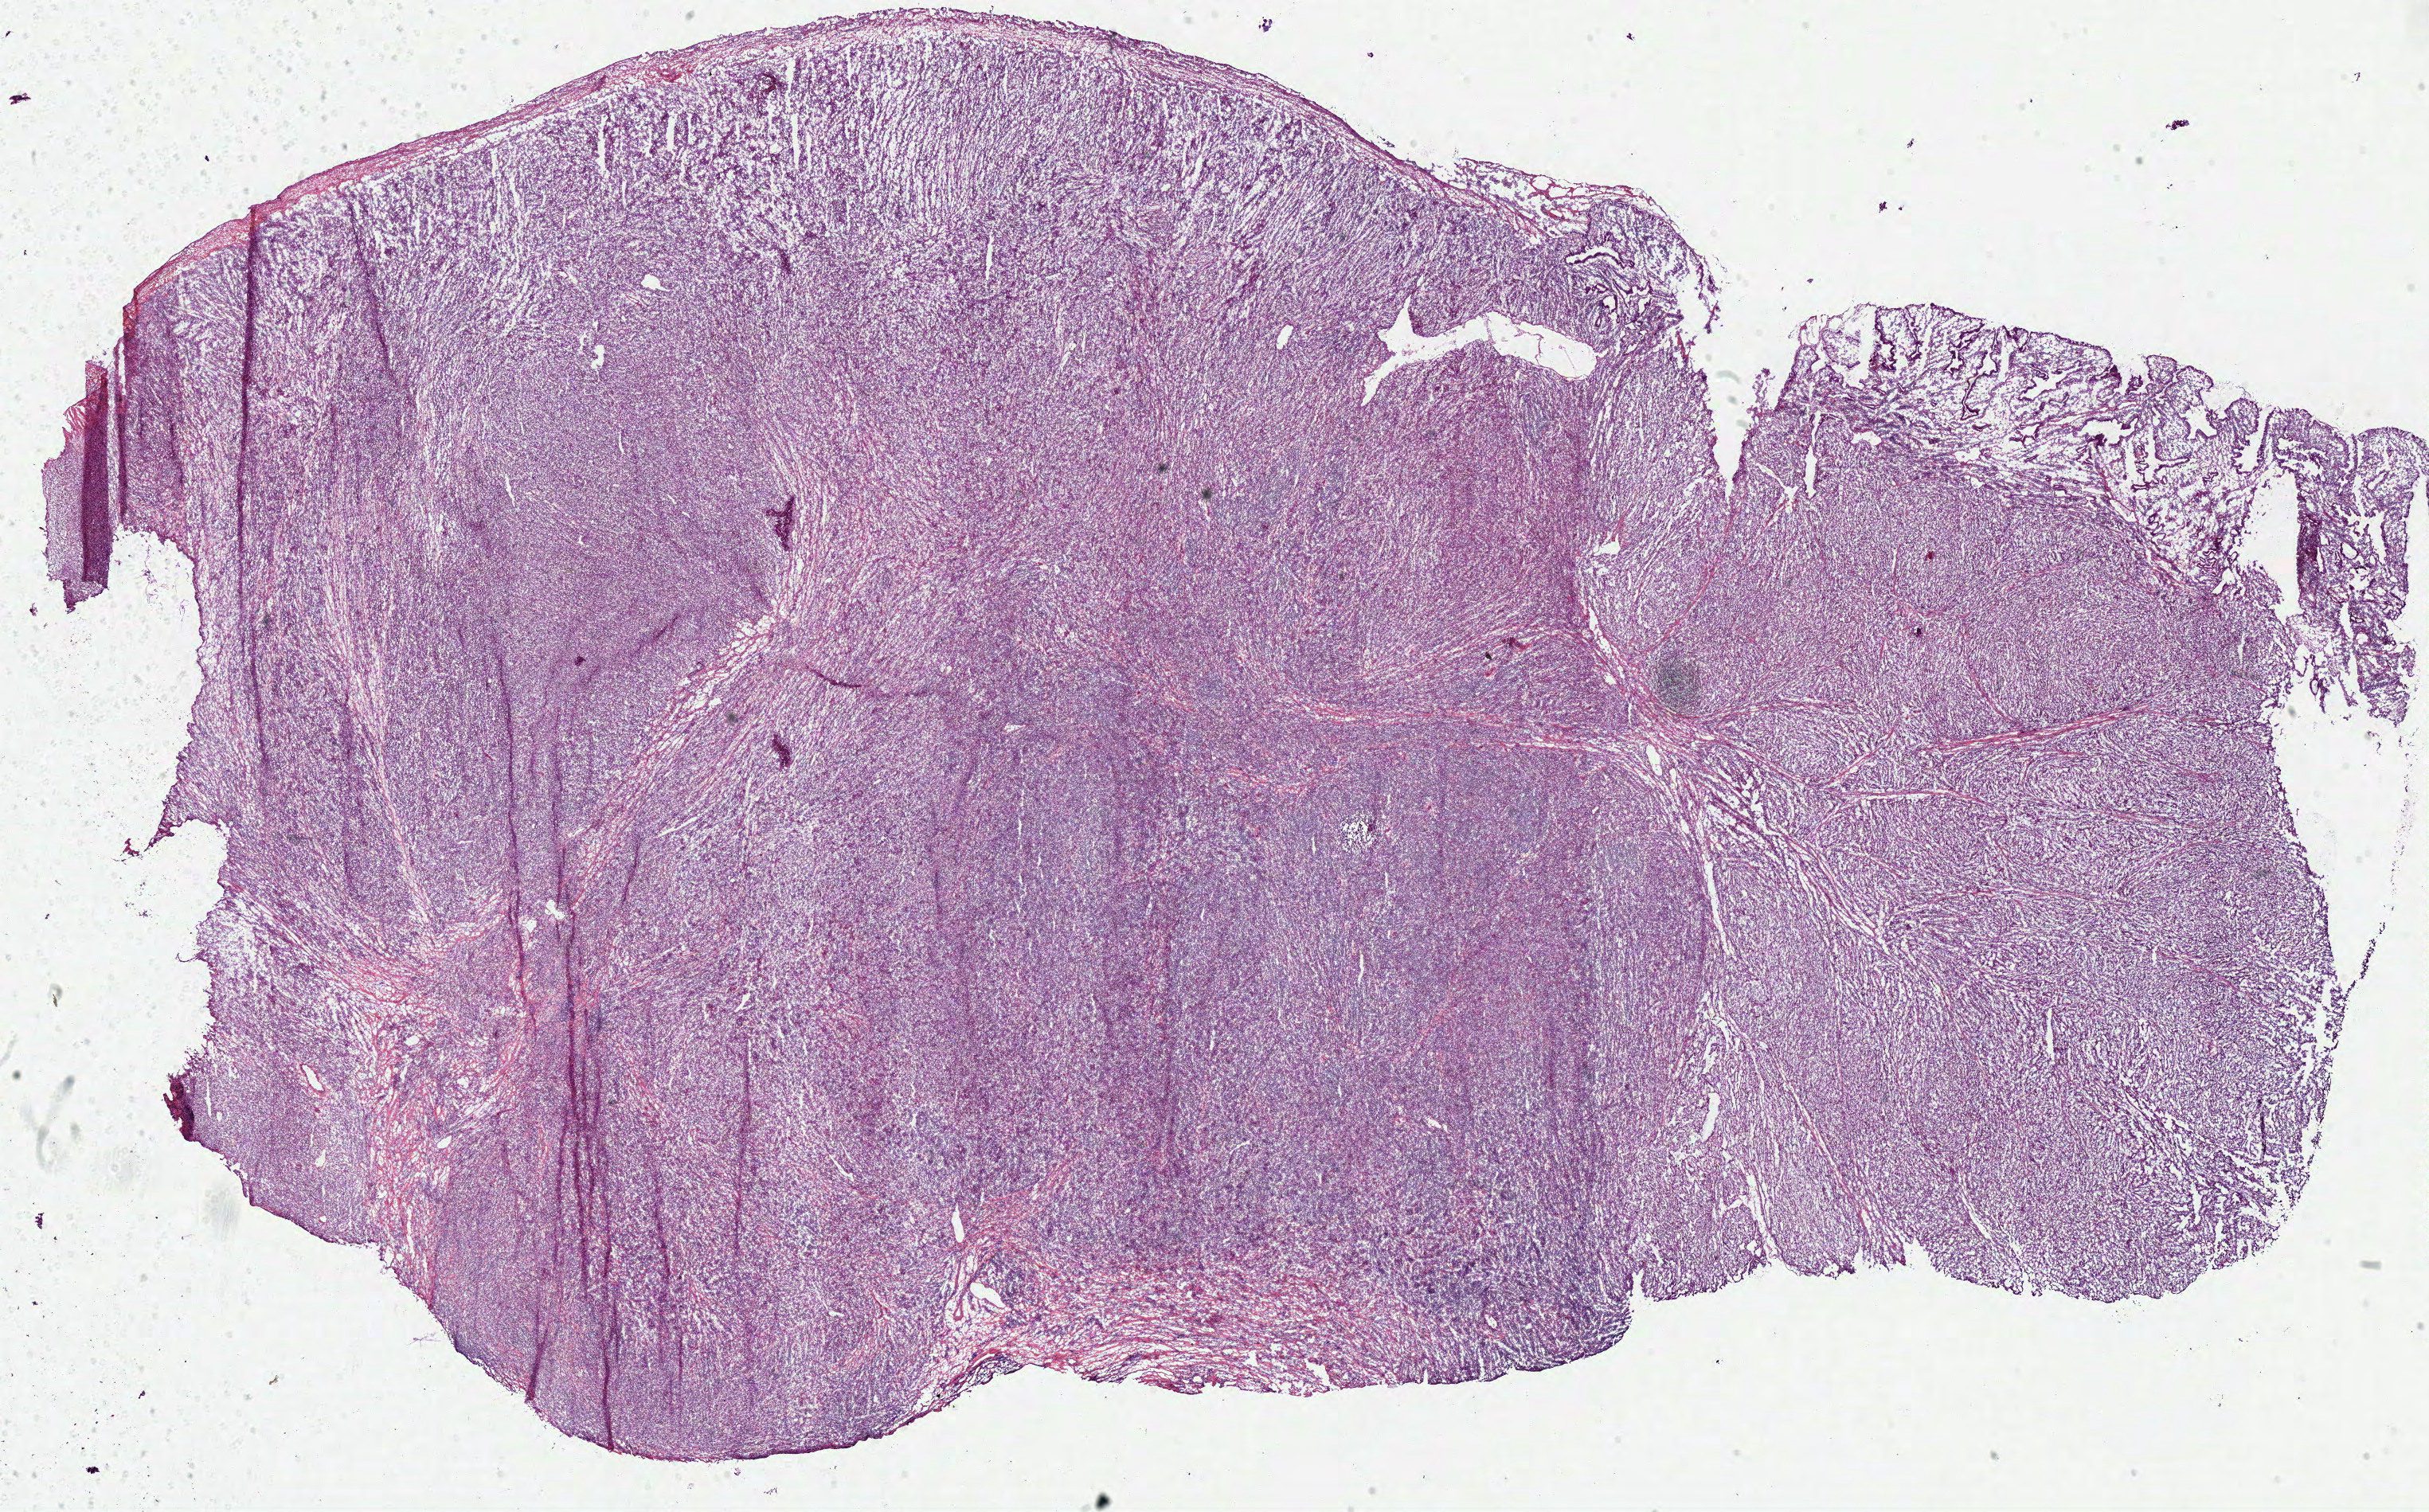
Whole-slide histology image, H&E-stained, shown as a low-resolution overview of the whole scanned area (about 24.0 x 14.9 mm, slide scanned at 40x). Frozen section from the bottom of the tissue portion. Primary tumour sample from the stomach. Female, age 57 years at initial diagnosis. Histologic grade: G3 (poorly differentiated). Slide review estimates, as recorded: tumour cells 85%, tumour nuclei 70%, normal cells 5%, stromal cells 10%, necrosis 0%.
* TNM: T3 N3a M0
* pathologic diagnosis: Adenocarcinoma, NOS (cardia, NOS)
* AJCC pathologic stage: IIIB